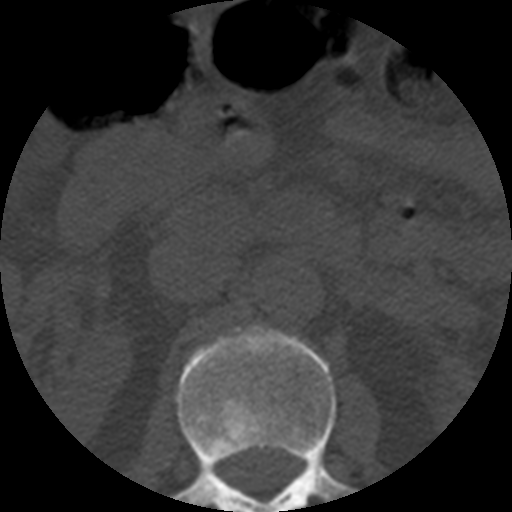
CT including the spine, one axial slice. Position 178 of 508 along the scan axis. 120 kVp. Bone window (W 1800 / L 400 HU). 512 × 512 image matrix. Patient age 57 years. Case-level facts recorded for this patient, not image findings: primary cancer: prostate.
Annotated regions visible in this slice (semi-automatic segmentation, software-assisted and operator-edited):
- L1 vertebra: bounding box (x1, y1, x2, y2) in pixels: (173, 326, 353, 512)